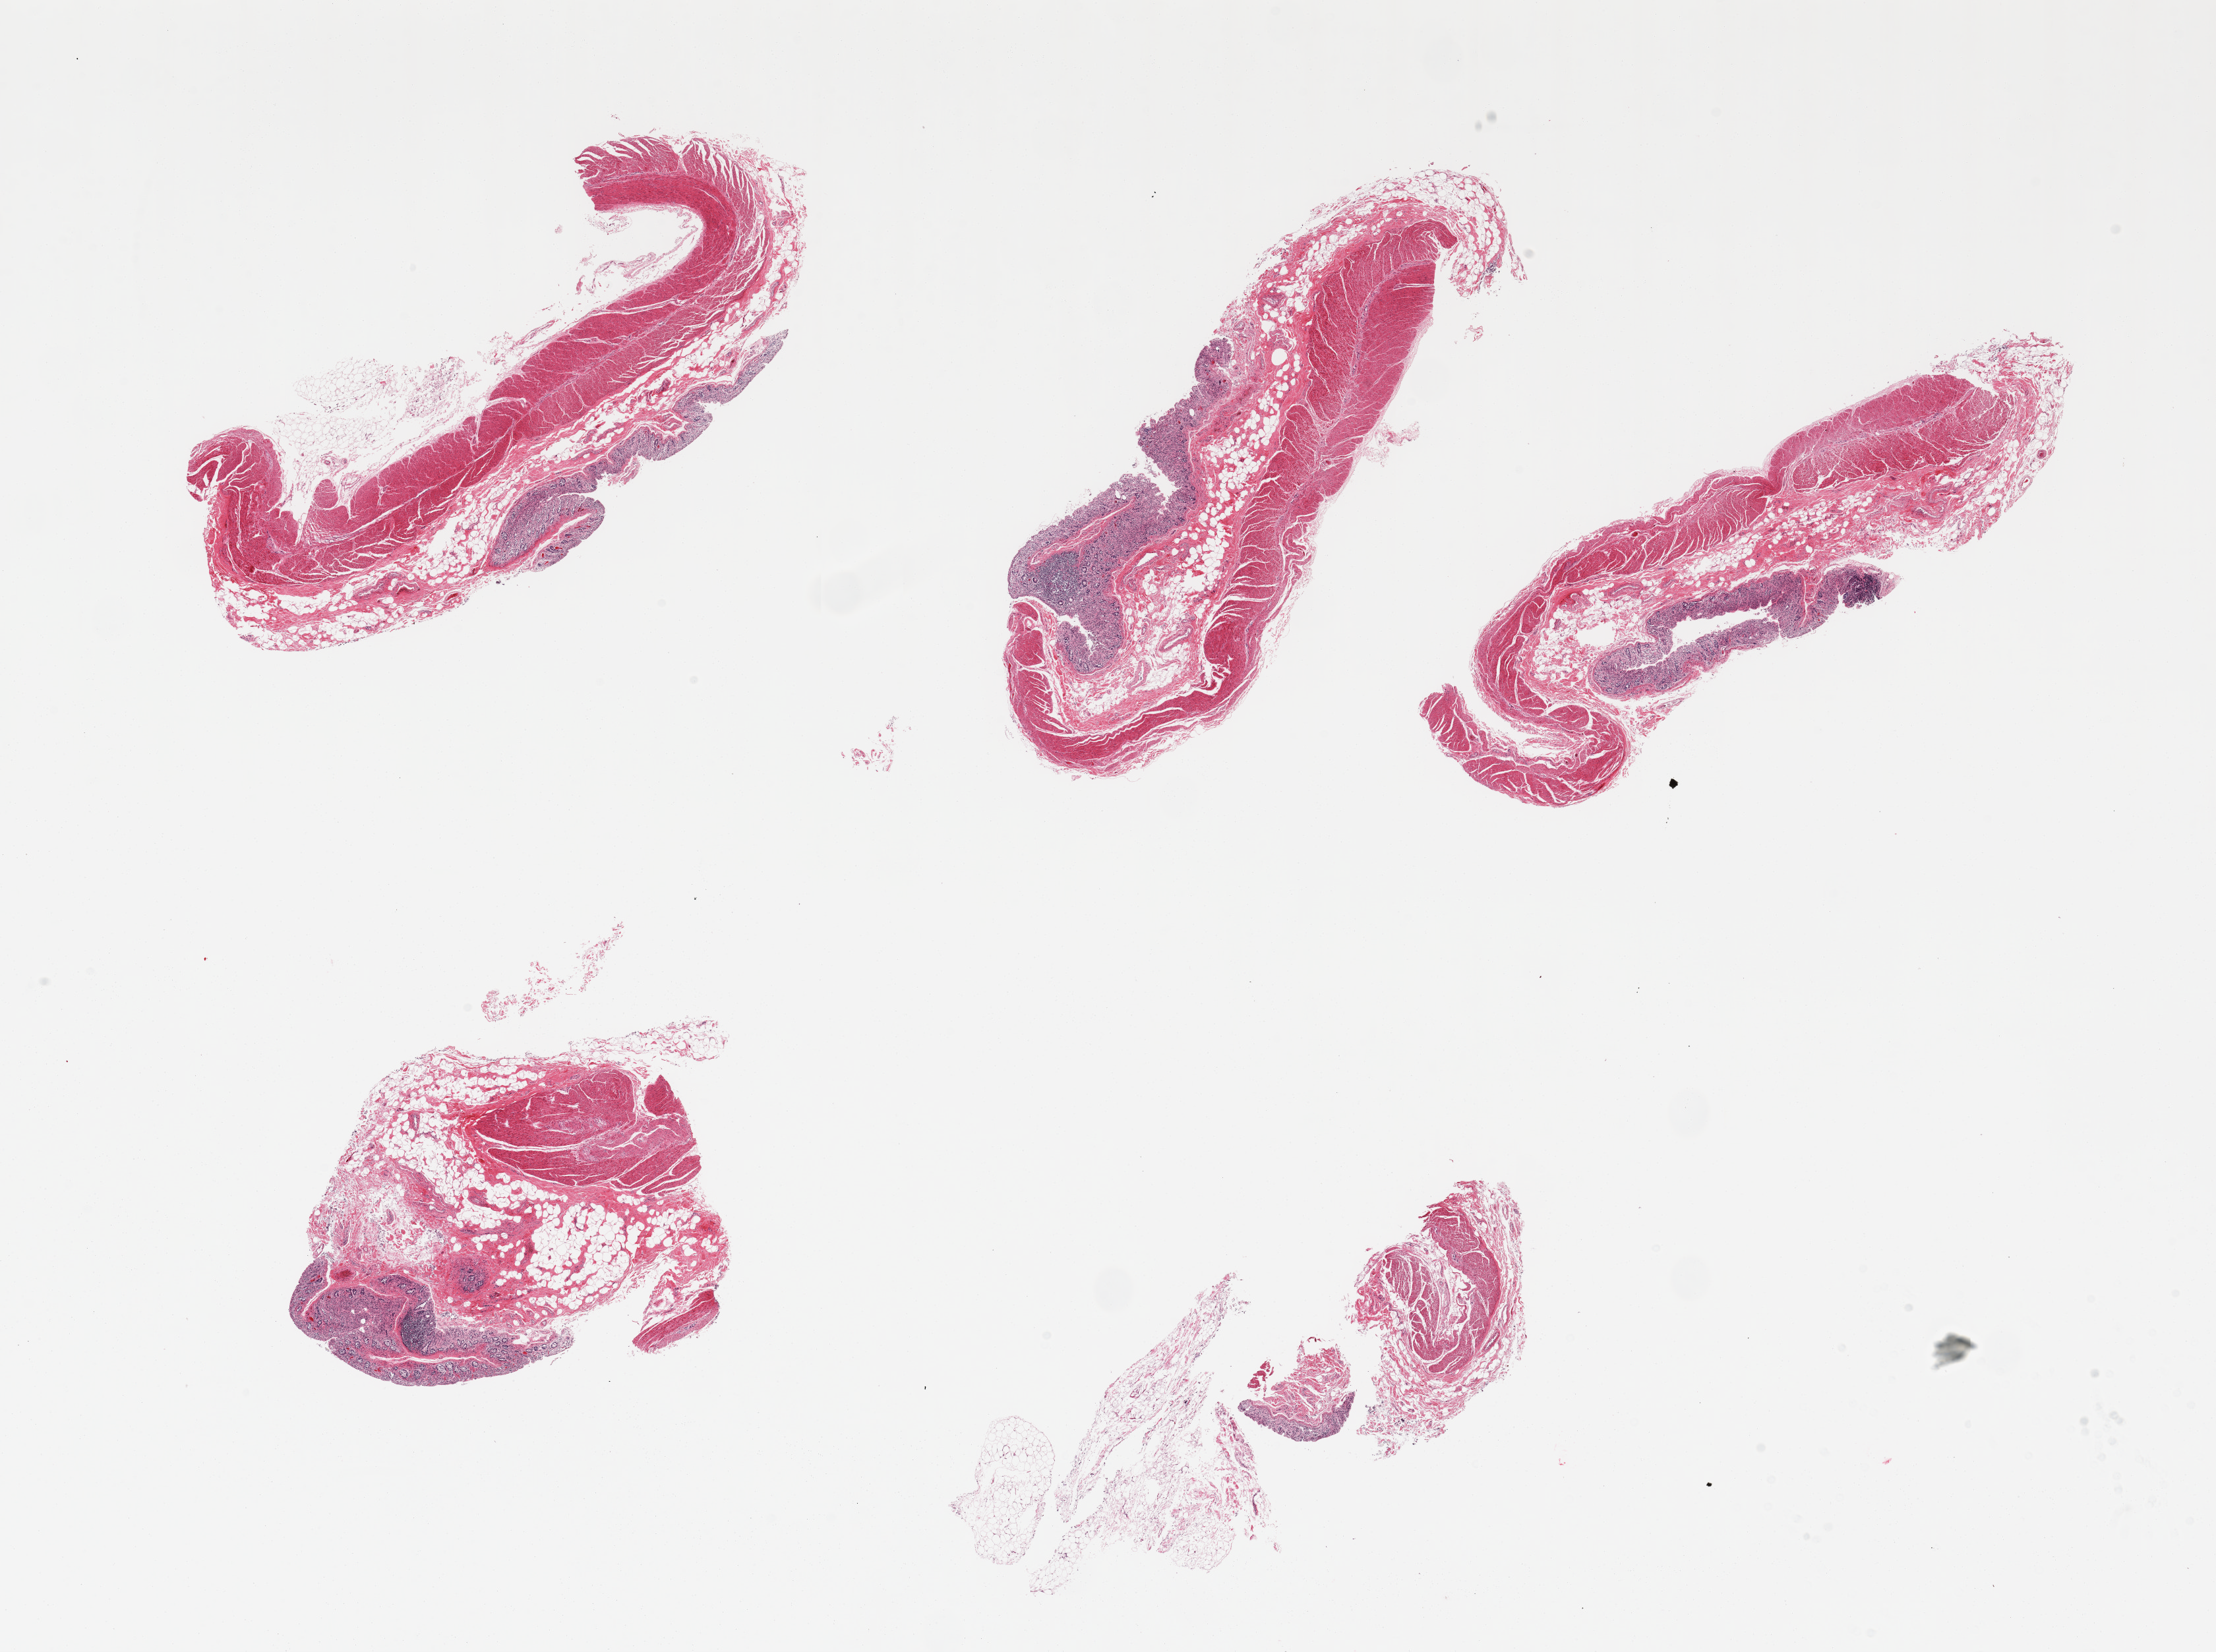
Haematoxylin and eosin whole-slide image, brightfield, a low-resolution overview of the entire scanned area, about 26.6 x 19.8 mm; PAXgene-fixed paraffin-embedded (PFPE) section; sampled site (target tissue): transverse colon; donor tissue sample.
* review note (as recorded): 5 pieces; mucosa autolyzed, muscularis preserved